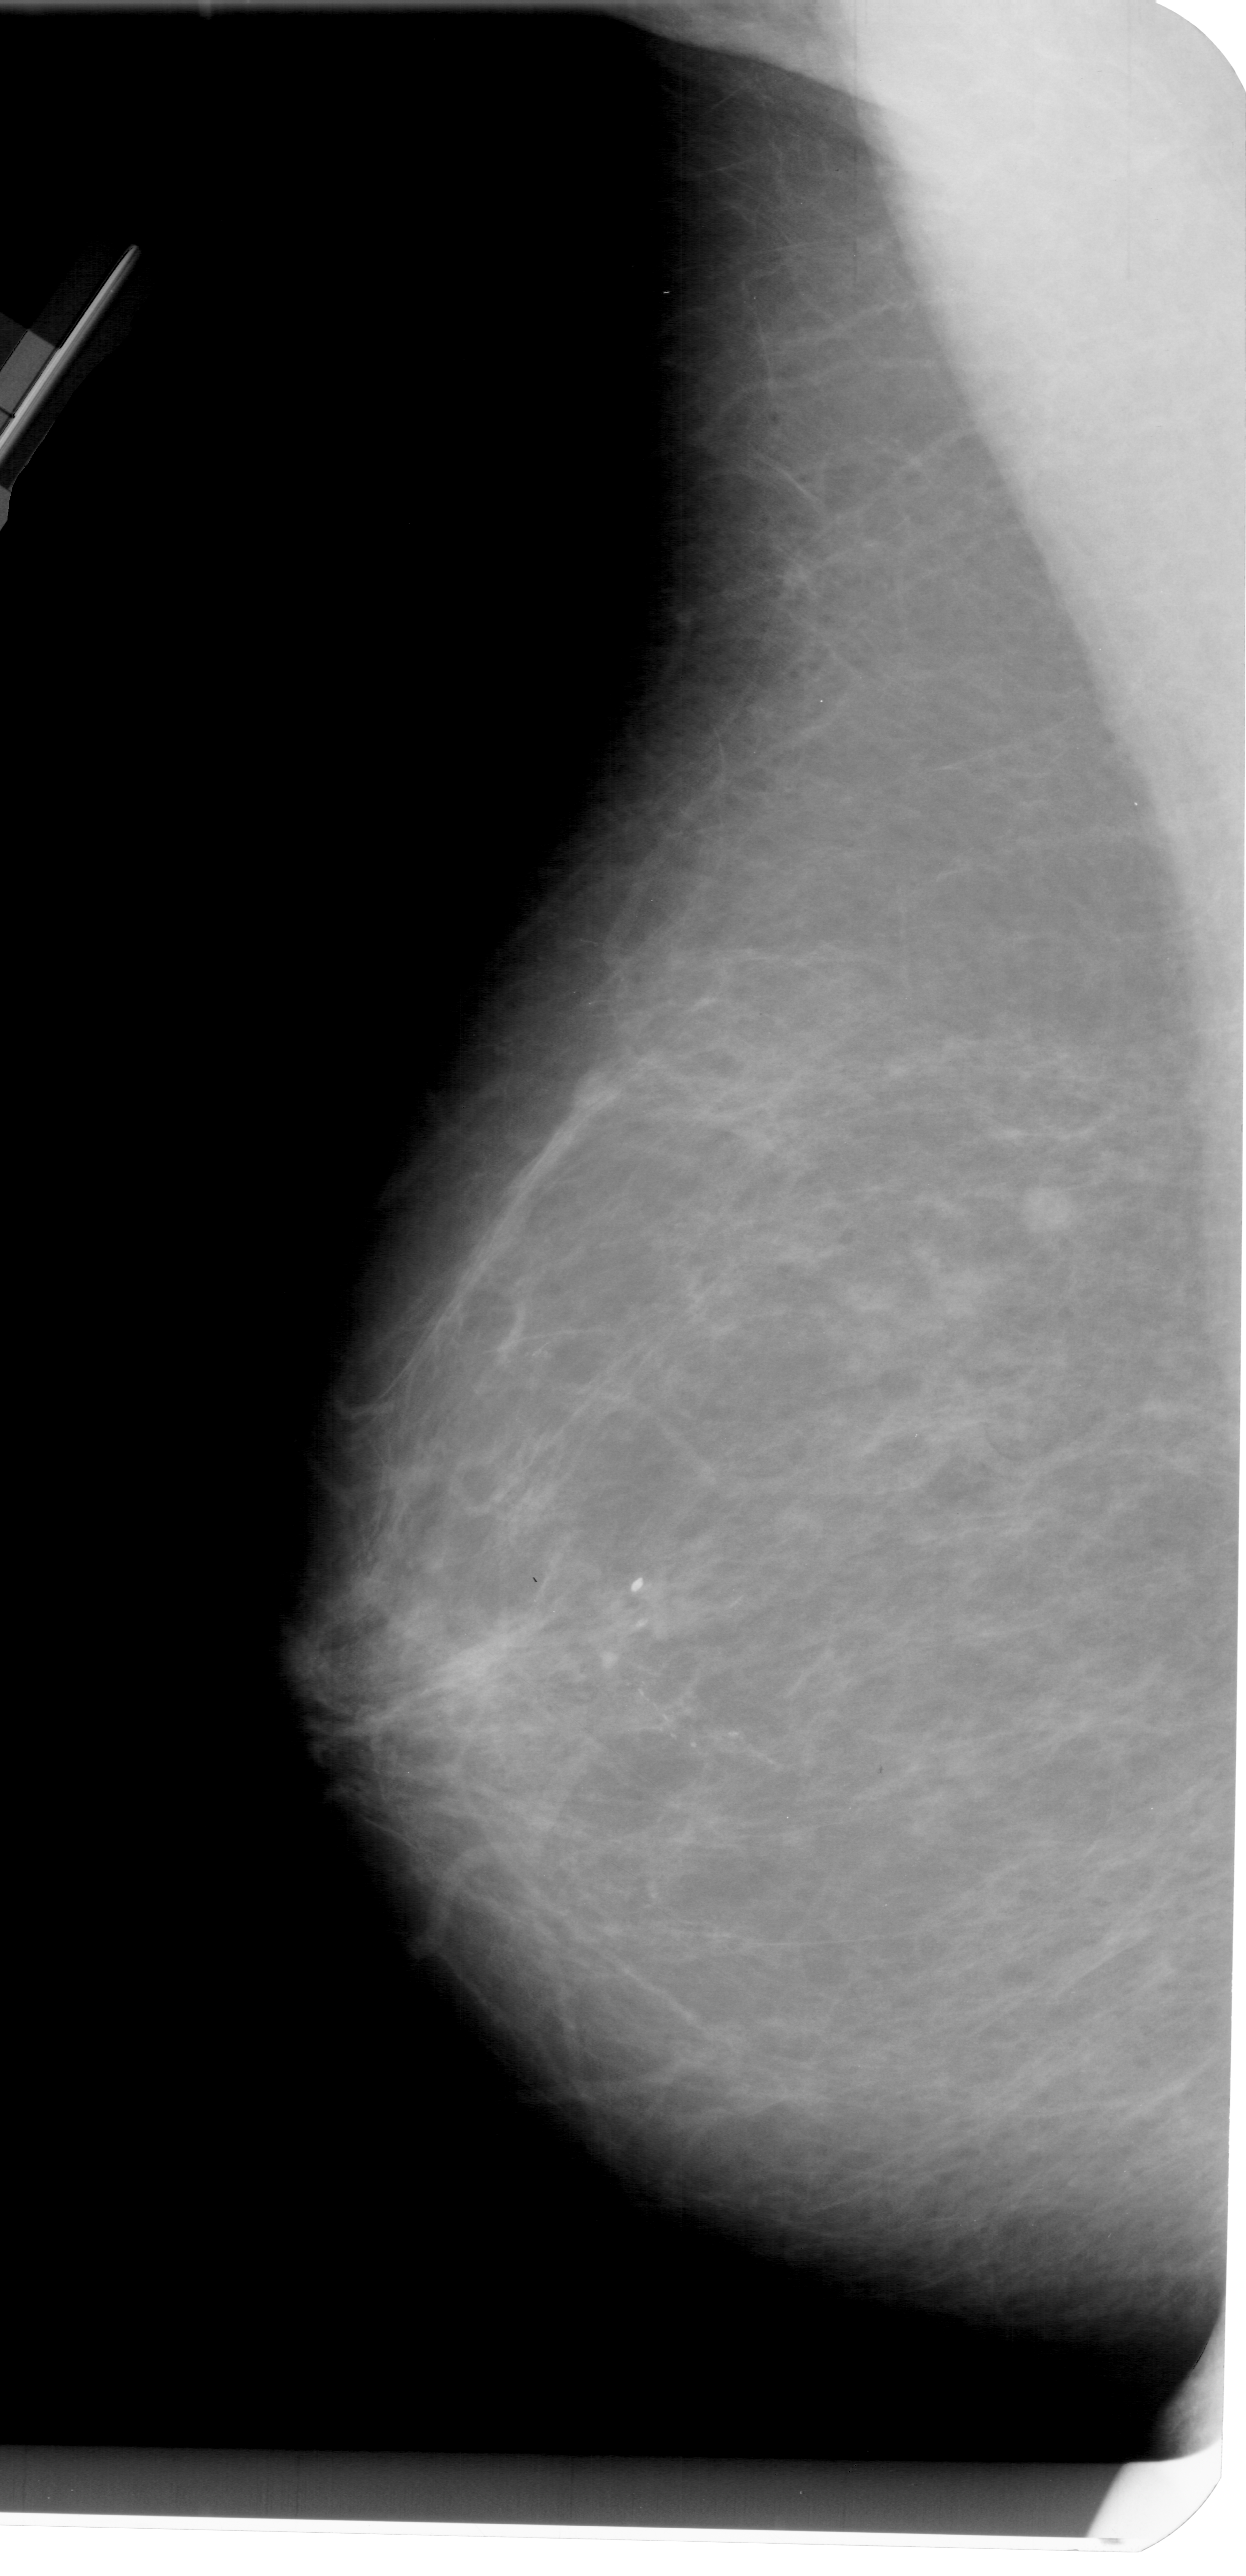
Mammogram (digitized film). Left breast. MLO view. Breast composition: scattered fibroglandular densities (BI-RADS density category 2 of 4). 1246 × 2576 image matrix.
Marked abnormalities (boxes around the expert regions of interest):
- calcifications, morphology pleomorphic, distribution linear; BI-RADS assessment category 4; pathology (as recorded): malignant: bounding box [x1, y1, x2, y2] px = [539, 1518, 826, 1801]